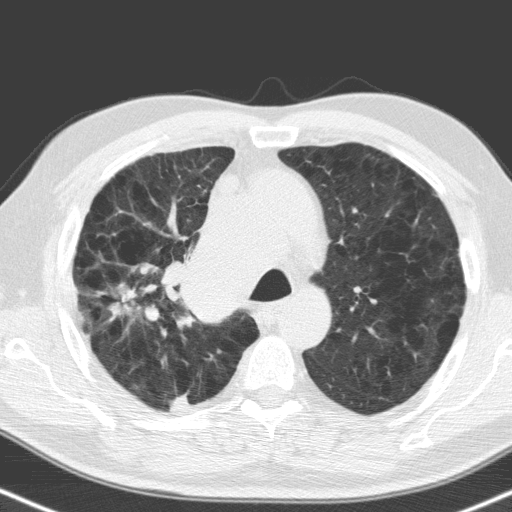
Chest CT (low-dose screening protocol), one axial image, baseline annual screen, lung window (W 1500 / L -600 HU), standard (soft-tissue) reconstruction kernel (C), 120 kVp, slice 43 of 160 in the series, 512 × 512 image matrix. Male participant, aged 71 years at enrolment.
• Lesion marked by an expert reader, bounding box [x1, y1, x2, y2] px = [96, 273, 178, 336].
• The screening reader recorded 2 non-calcified nodules or masses ≥4 mm on this exam (right upper lobe, right upper lobe); which of them this box marks is not recorded.
• Later outcome: lung cancer diagnosed 31 days after this screen — small cell carcinoma, NOS, right upper lobe, stage IV (AJCC 6th edition), 40 mm at pathology.